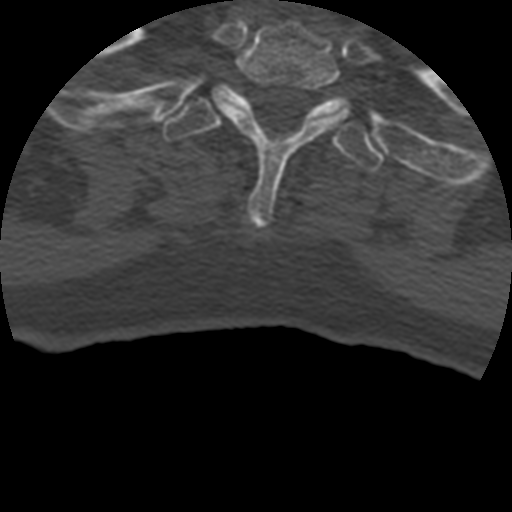
CT including the spine, one axial slice. Position 377 of 399 along the scan axis. 120 kVp. Bone window (W 1800 / L 400 HU). 1.25 mm slice thickness. 512 × 512 image matrix, field of view 160 × 160 mm. Patient age 69 years. Case-level facts recorded for this patient, not image findings: primary cancer: prostate.
Structures marked on this image (semi-automatic segmentation, software-assisted and operator-edited):
- T1 vertebra: bounding box [x1, y1, x2, y2] px = [206, 22, 355, 225]
- T2 vertebra: [163, 84, 383, 171]